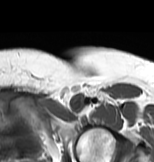
MRI of an extremity soft-tissue mass, one axial slice; slice 62 of 83 in the series (ordered by position); MR volume resampled by the dataset authors to the PET/CT grid (not the native acquisition matrix); 3.27 mm slice thickness; 154 × 162 image matrix. Female patient. From the clinical record (not read from this slice): histological type: myxofibrosarcoma; grade: intermediate; site of the primary tumour: left thigh.
Outlined on this slice (expert contour drawn on MRI and transferred to this co-registered scan by the dataset authors):
- gross tumour volume including surrounding oedema: bounding box <69,96,88,115> (left, top, right, bottom; pixels)